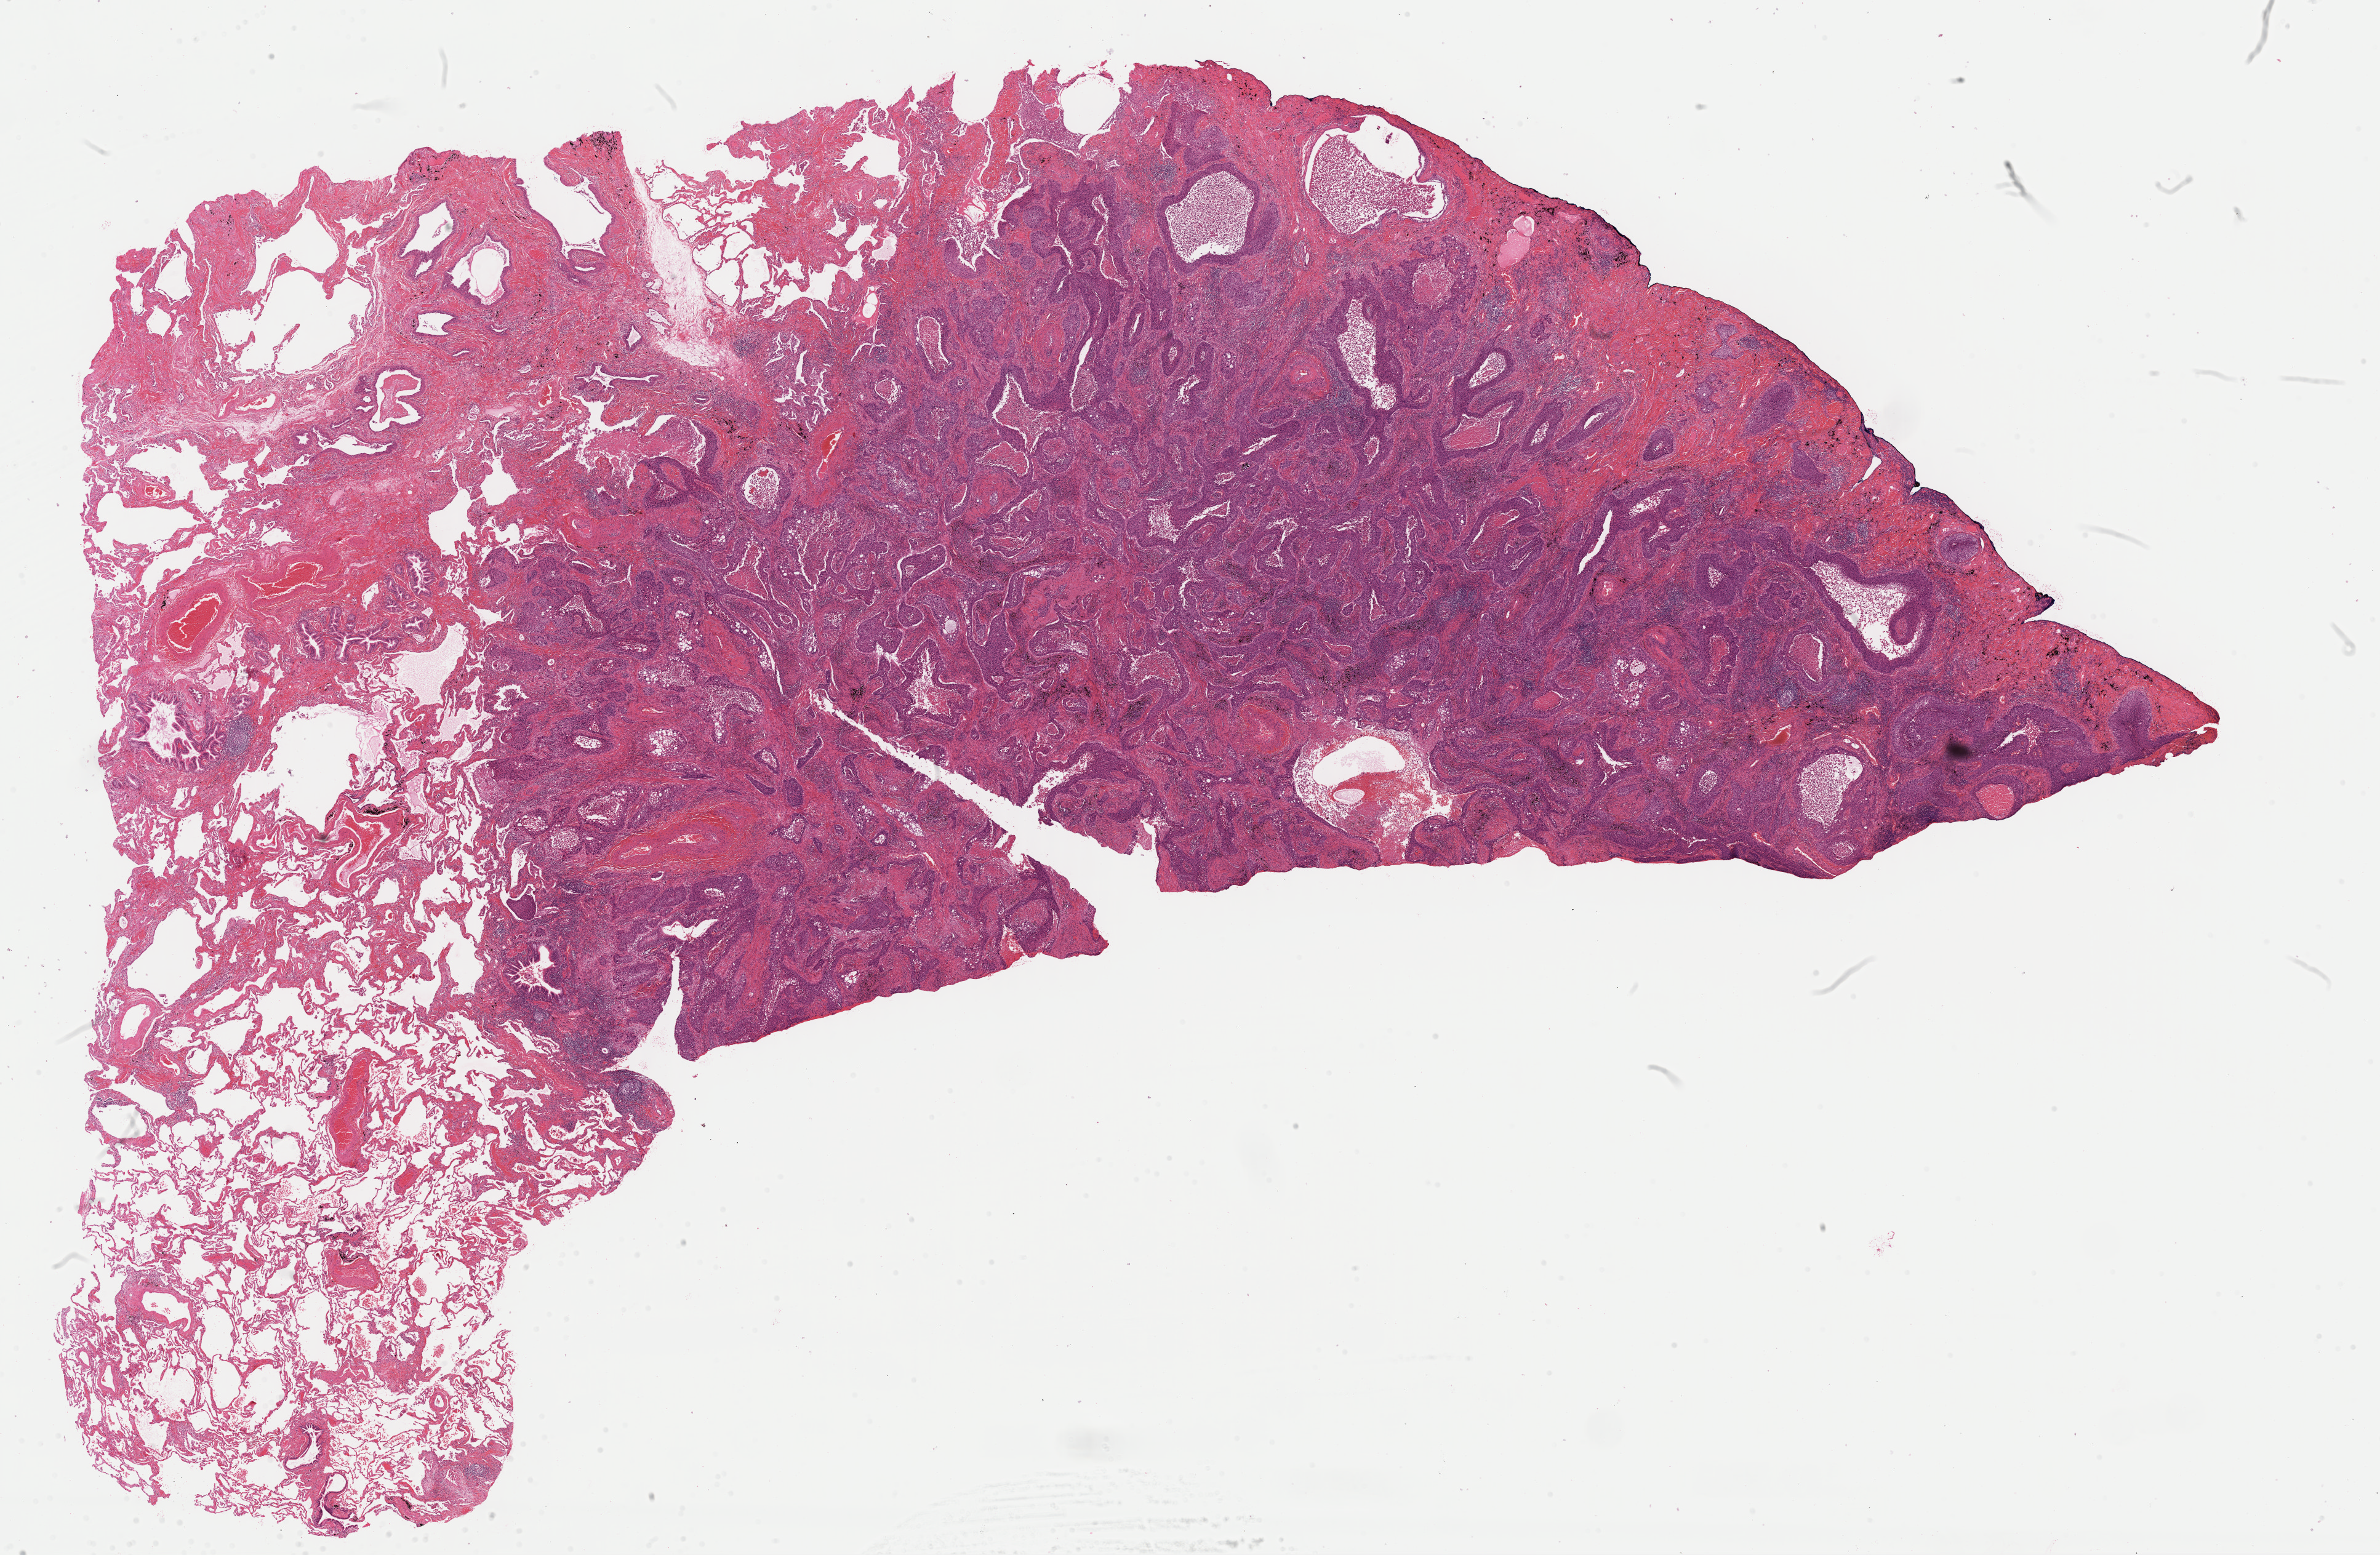
Digitized H&E-stained tissue section (whole slide), low-resolution overview of the scanned area, about 30.5 x 20.0 mm, formalin-fixed paraffin-embedded (FFPE) diagnostic section, primary tumour sample from the lung. Male, age 70 years at initial diagnosis.
TNM: T2a N1 M0. Laterality: left. Diagnosis: Squamous cell carcinoma, NOS (lower lobe, lung). AJCC pathologic stage: IIA (7th edition).